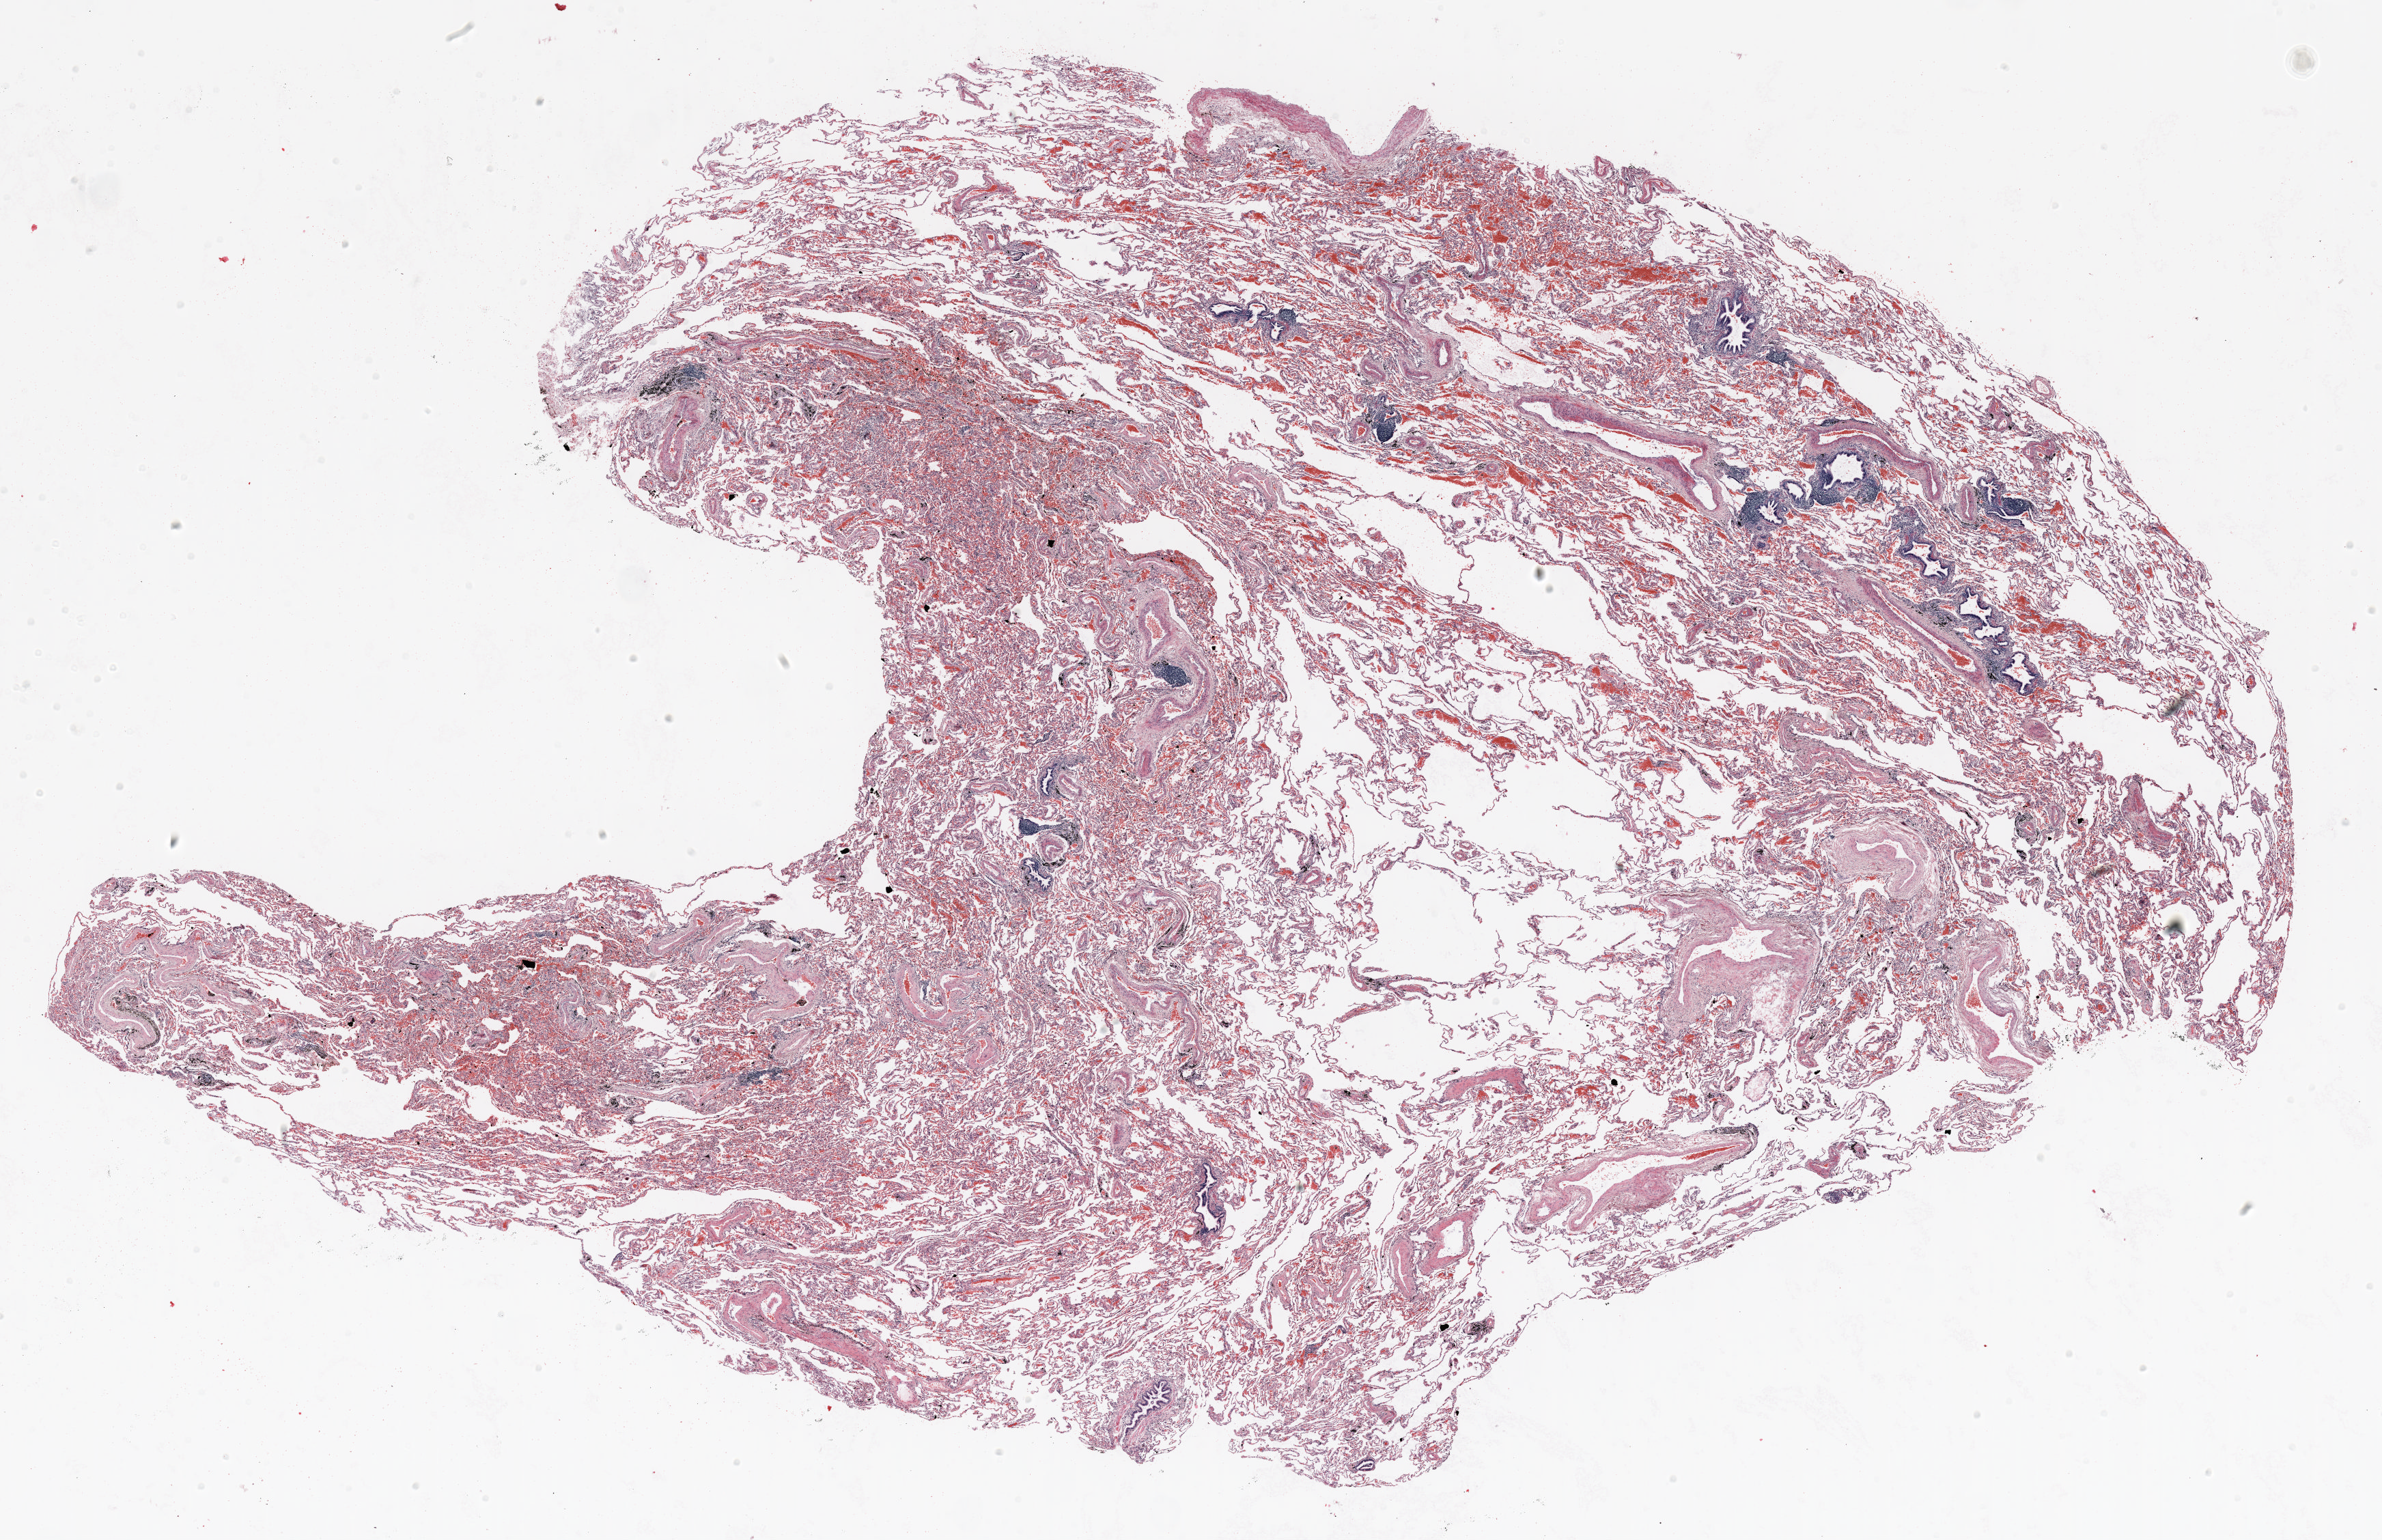
Whole-slide histology image, H&E — low-resolution overview of the scanned area, about 28.0 x 18.1 mm (acquisition: 20x scan). Formalin-fixed paraffin-embedded (FFPE) section. Lung tissue. Male patient, aged 63 at enrolment. Current smoker at enrolment. Grade: poorly differentiated (G3).
Stage (AJCC 6th edition): IA. Tumour size (pathology): 4 mm. Participant's lung-cancer diagnosis: Squamous cell carcinoma, NOS. Primary tumour location (clinical record): left lower lobe.